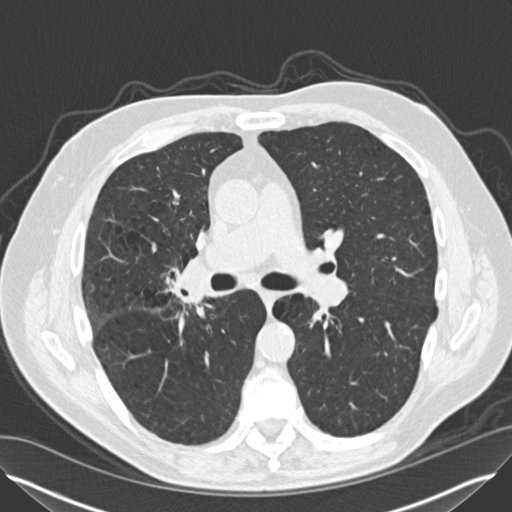
Low-dose screening chest CT, axial slice. Second screening round (one year after baseline). Lung window (W 1500 / L -600 HU). Slice 67 of 149 in the series. Male participant, aged 65 years at enrolment.
Expert reader's lesion annotation, bounding box (x1, y1, x2, y2) in pixels: (157, 262, 214, 315). The exam's reader record, not a measurement of the box and not confirmed to be the same lesion: non-calcified nodule or mass ≥4 mm, left lower lobe, 12 × 8 mm, smooth margins, soft tissue attenuation, pre-existing on the prior screen: yes; interval growth: yes. Note: the box lies in the patient's right hemithorax on this image, whereas the reader's record names the left lung; they may be different findings. Official screen result: positive, other. Lung cancer was diagnosed 67 days after this screen: non-small cell carcinoma, left lower lobe, right hilum, poorly differentiated (G3), stage IV (AJCC 6th edition), 5 mm at pathology.